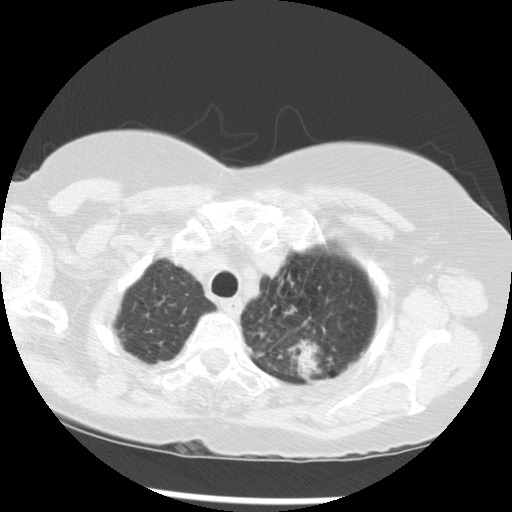
Low-dose screening chest CT, one axial slice; slice 244 of 283 in the series (ordered by position); 120 kVp; lung window (W 1500 / L -600 HU); 2.5 mm slice thickness; 512 × 512 image matrix.
Outlined on this slice (outlined manually by an expert reader):
- lesion 1 (tumor, upper lobe of left lung): bounding box [x1, y1, x2, y2] px = [289, 341, 321, 377]